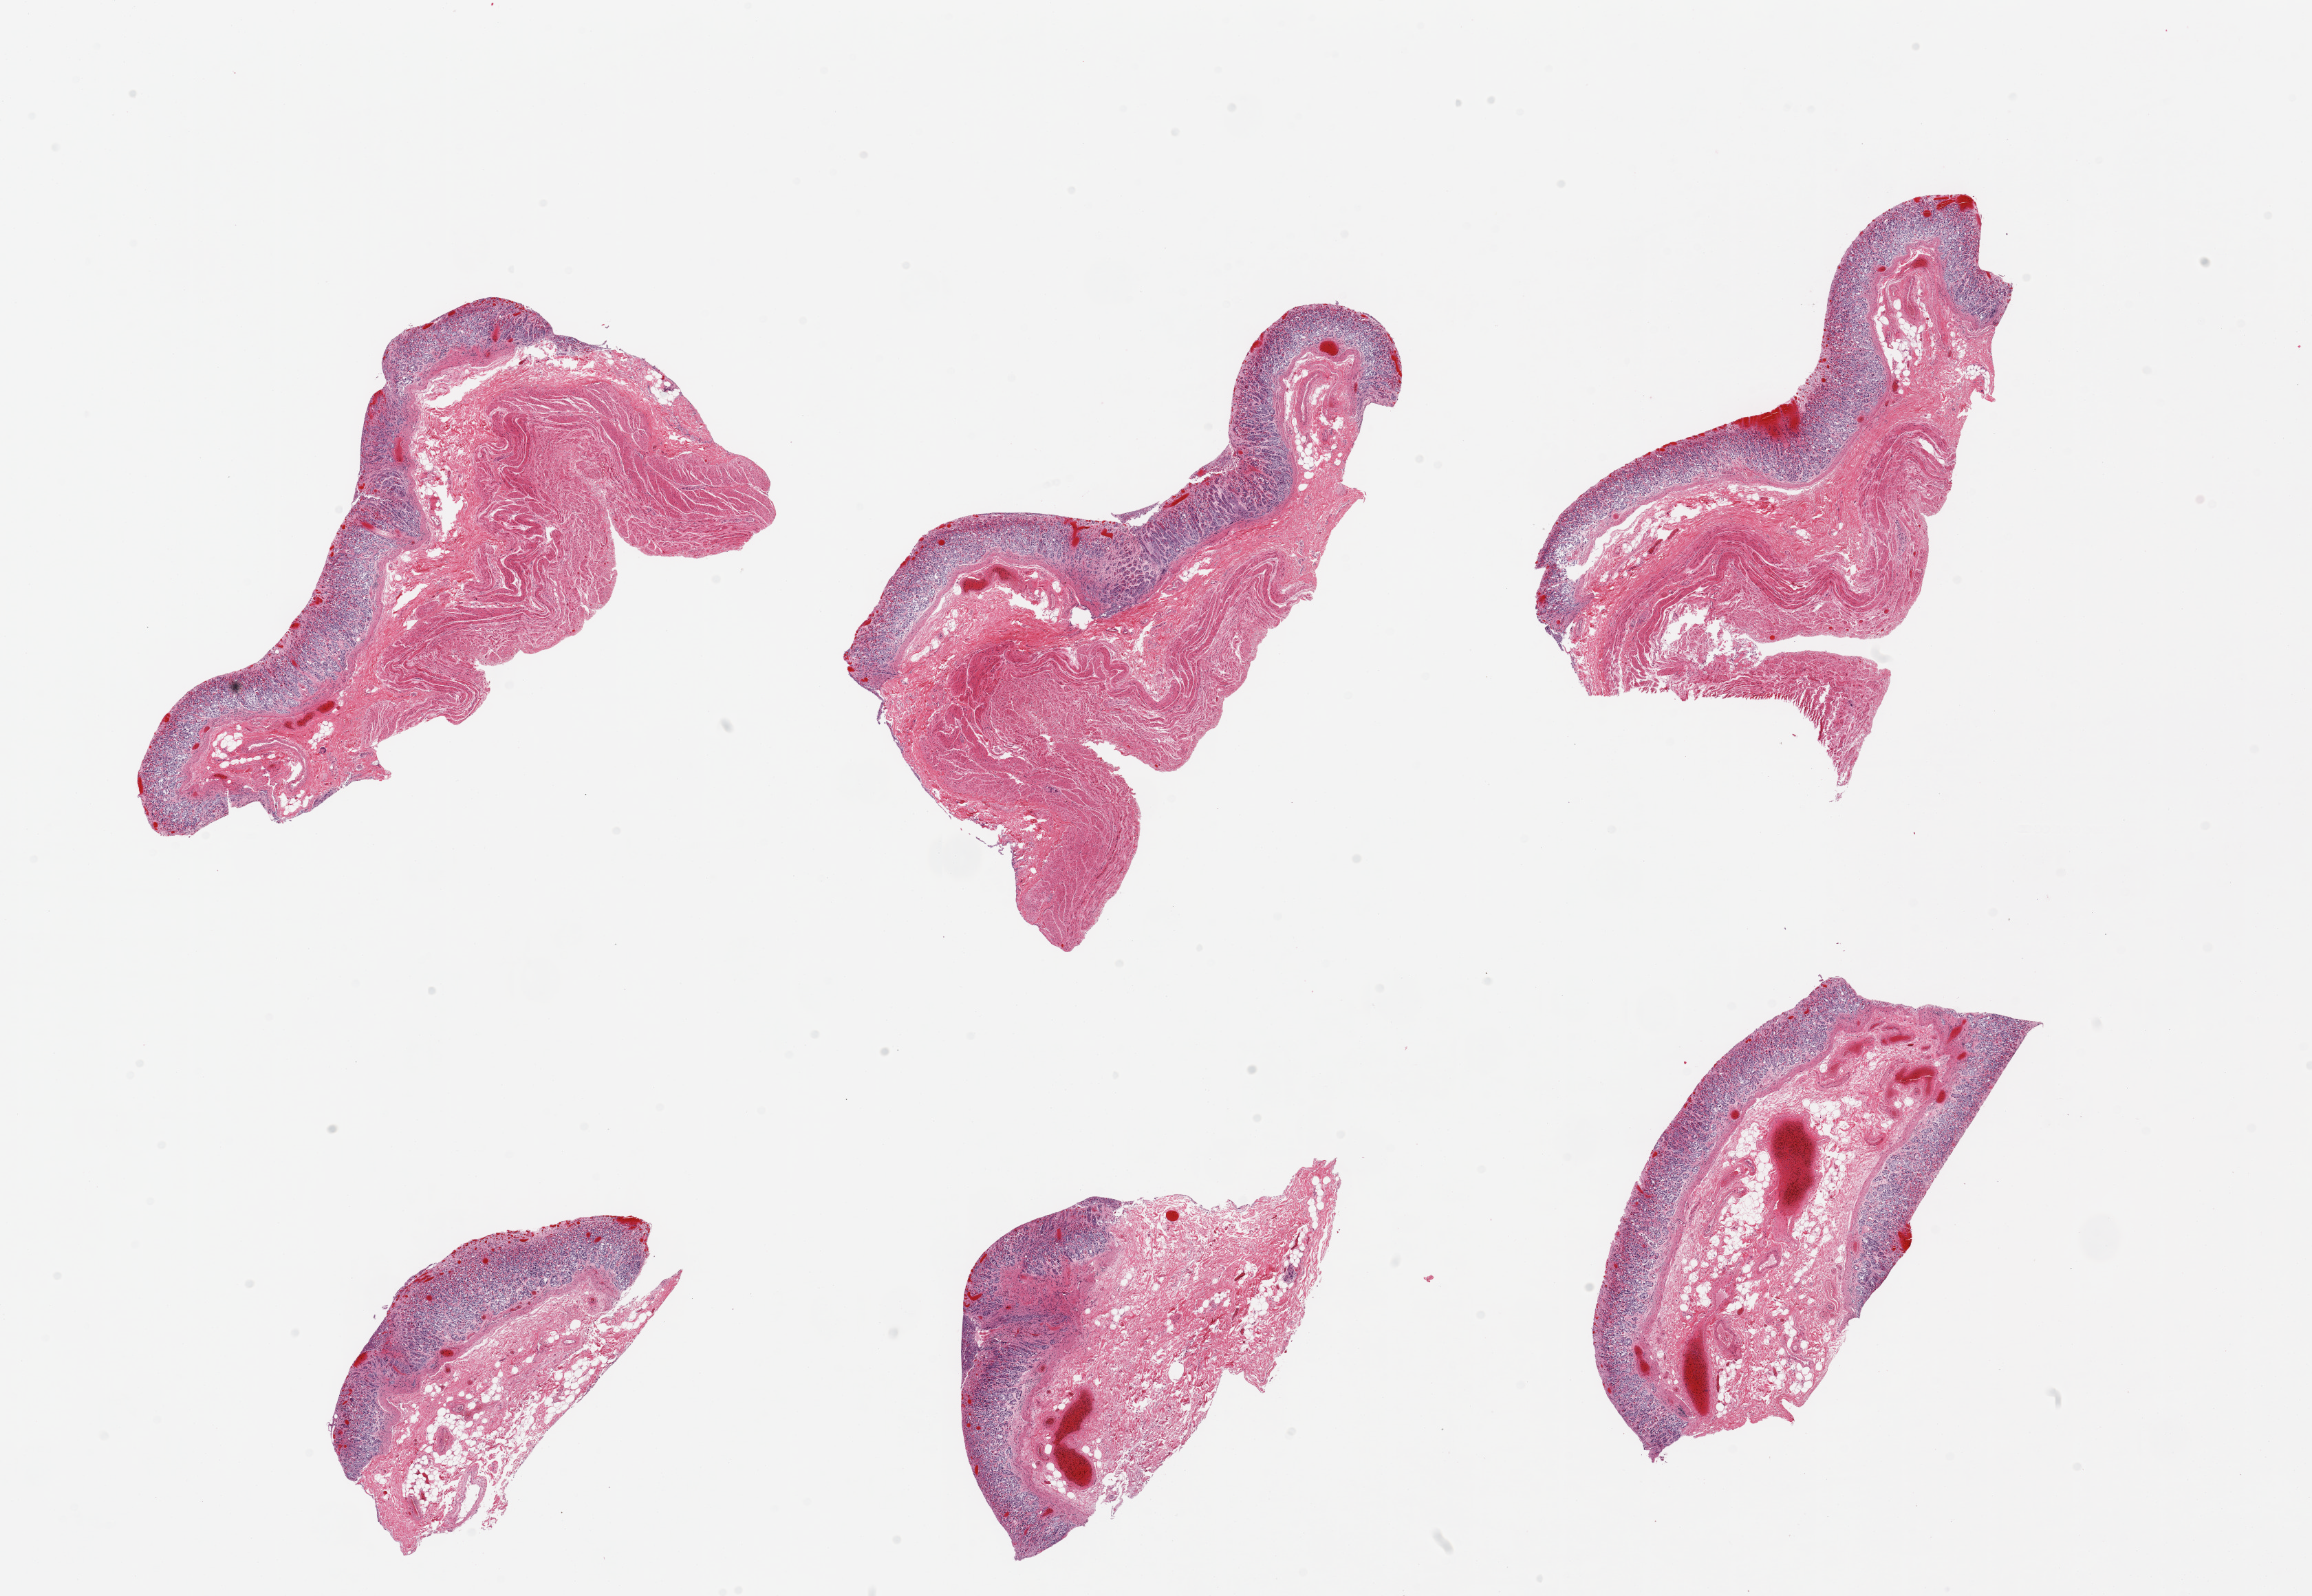
Digitized haematoxylin and eosin-stained section — a low-resolution overview of the entire scanned area, about 26.6 x 18.3 mm; PAXgene-fixed, paraffin-embedded tissue; sampled site (target tissue): stomach; tissue donor sample. Male donor.
- review note (as recorded): 6 pieces; 3 include mucosa and muscularis, 3 are mucosa/submucosa only